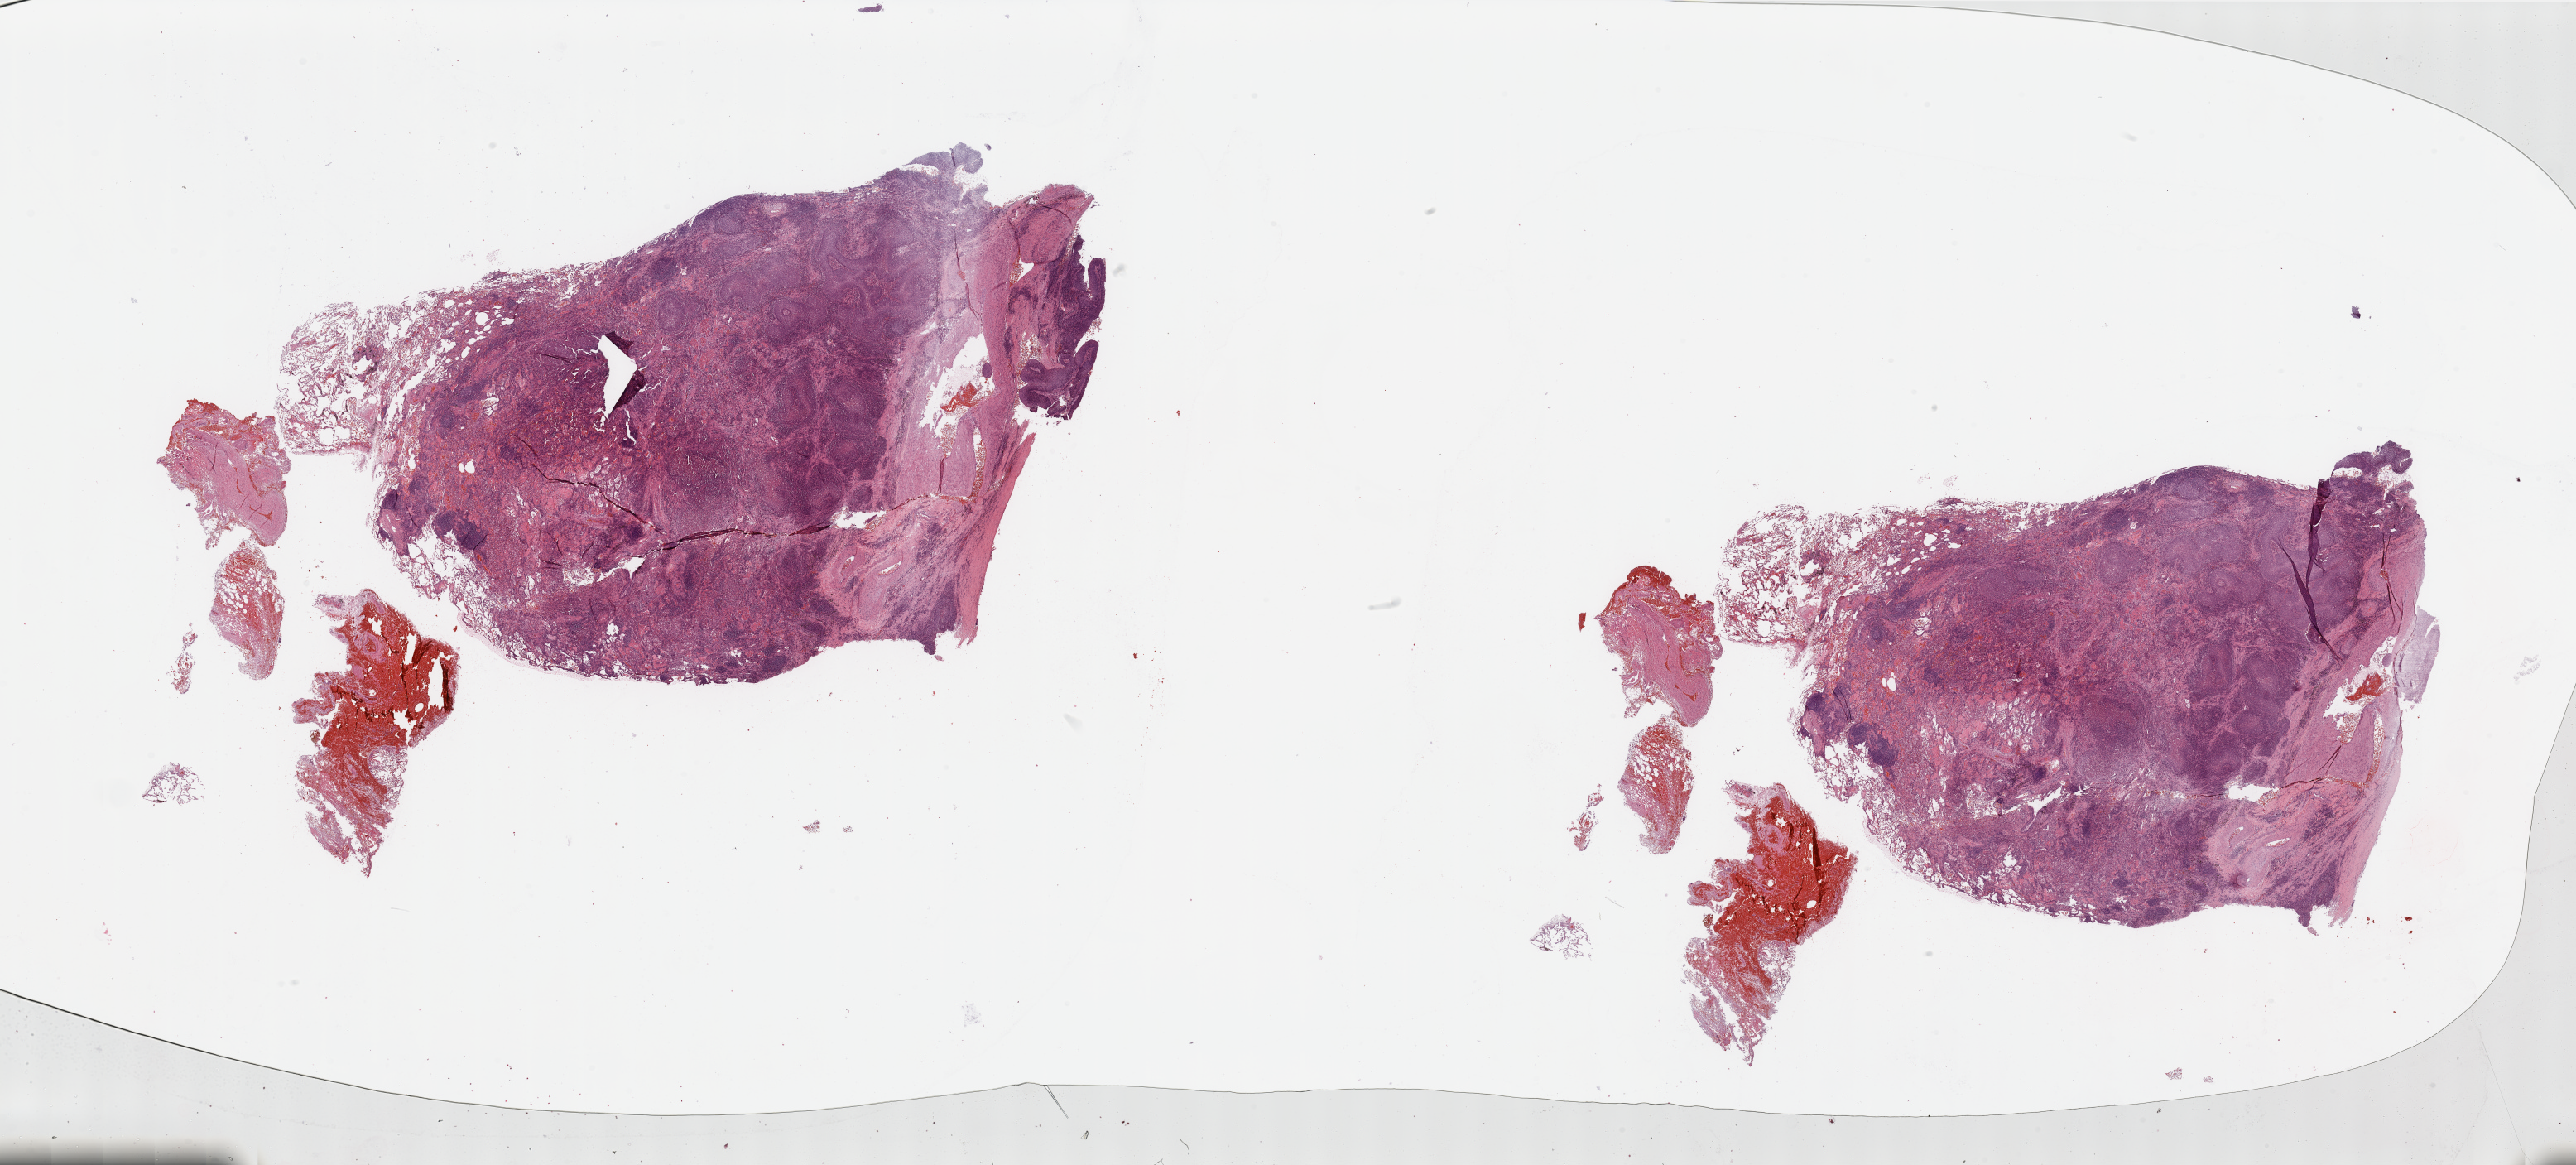
Digitized H&E tissue section (whole slide), a low-resolution overview of the entire scanned area, about 49.2 x 22.3 mm (slide scanned at 20x). Tumour tissue sample, lung. Male, 68 y/o.
- patient diagnosis (cohort enrolment): squamous cell carcinoma (lung)